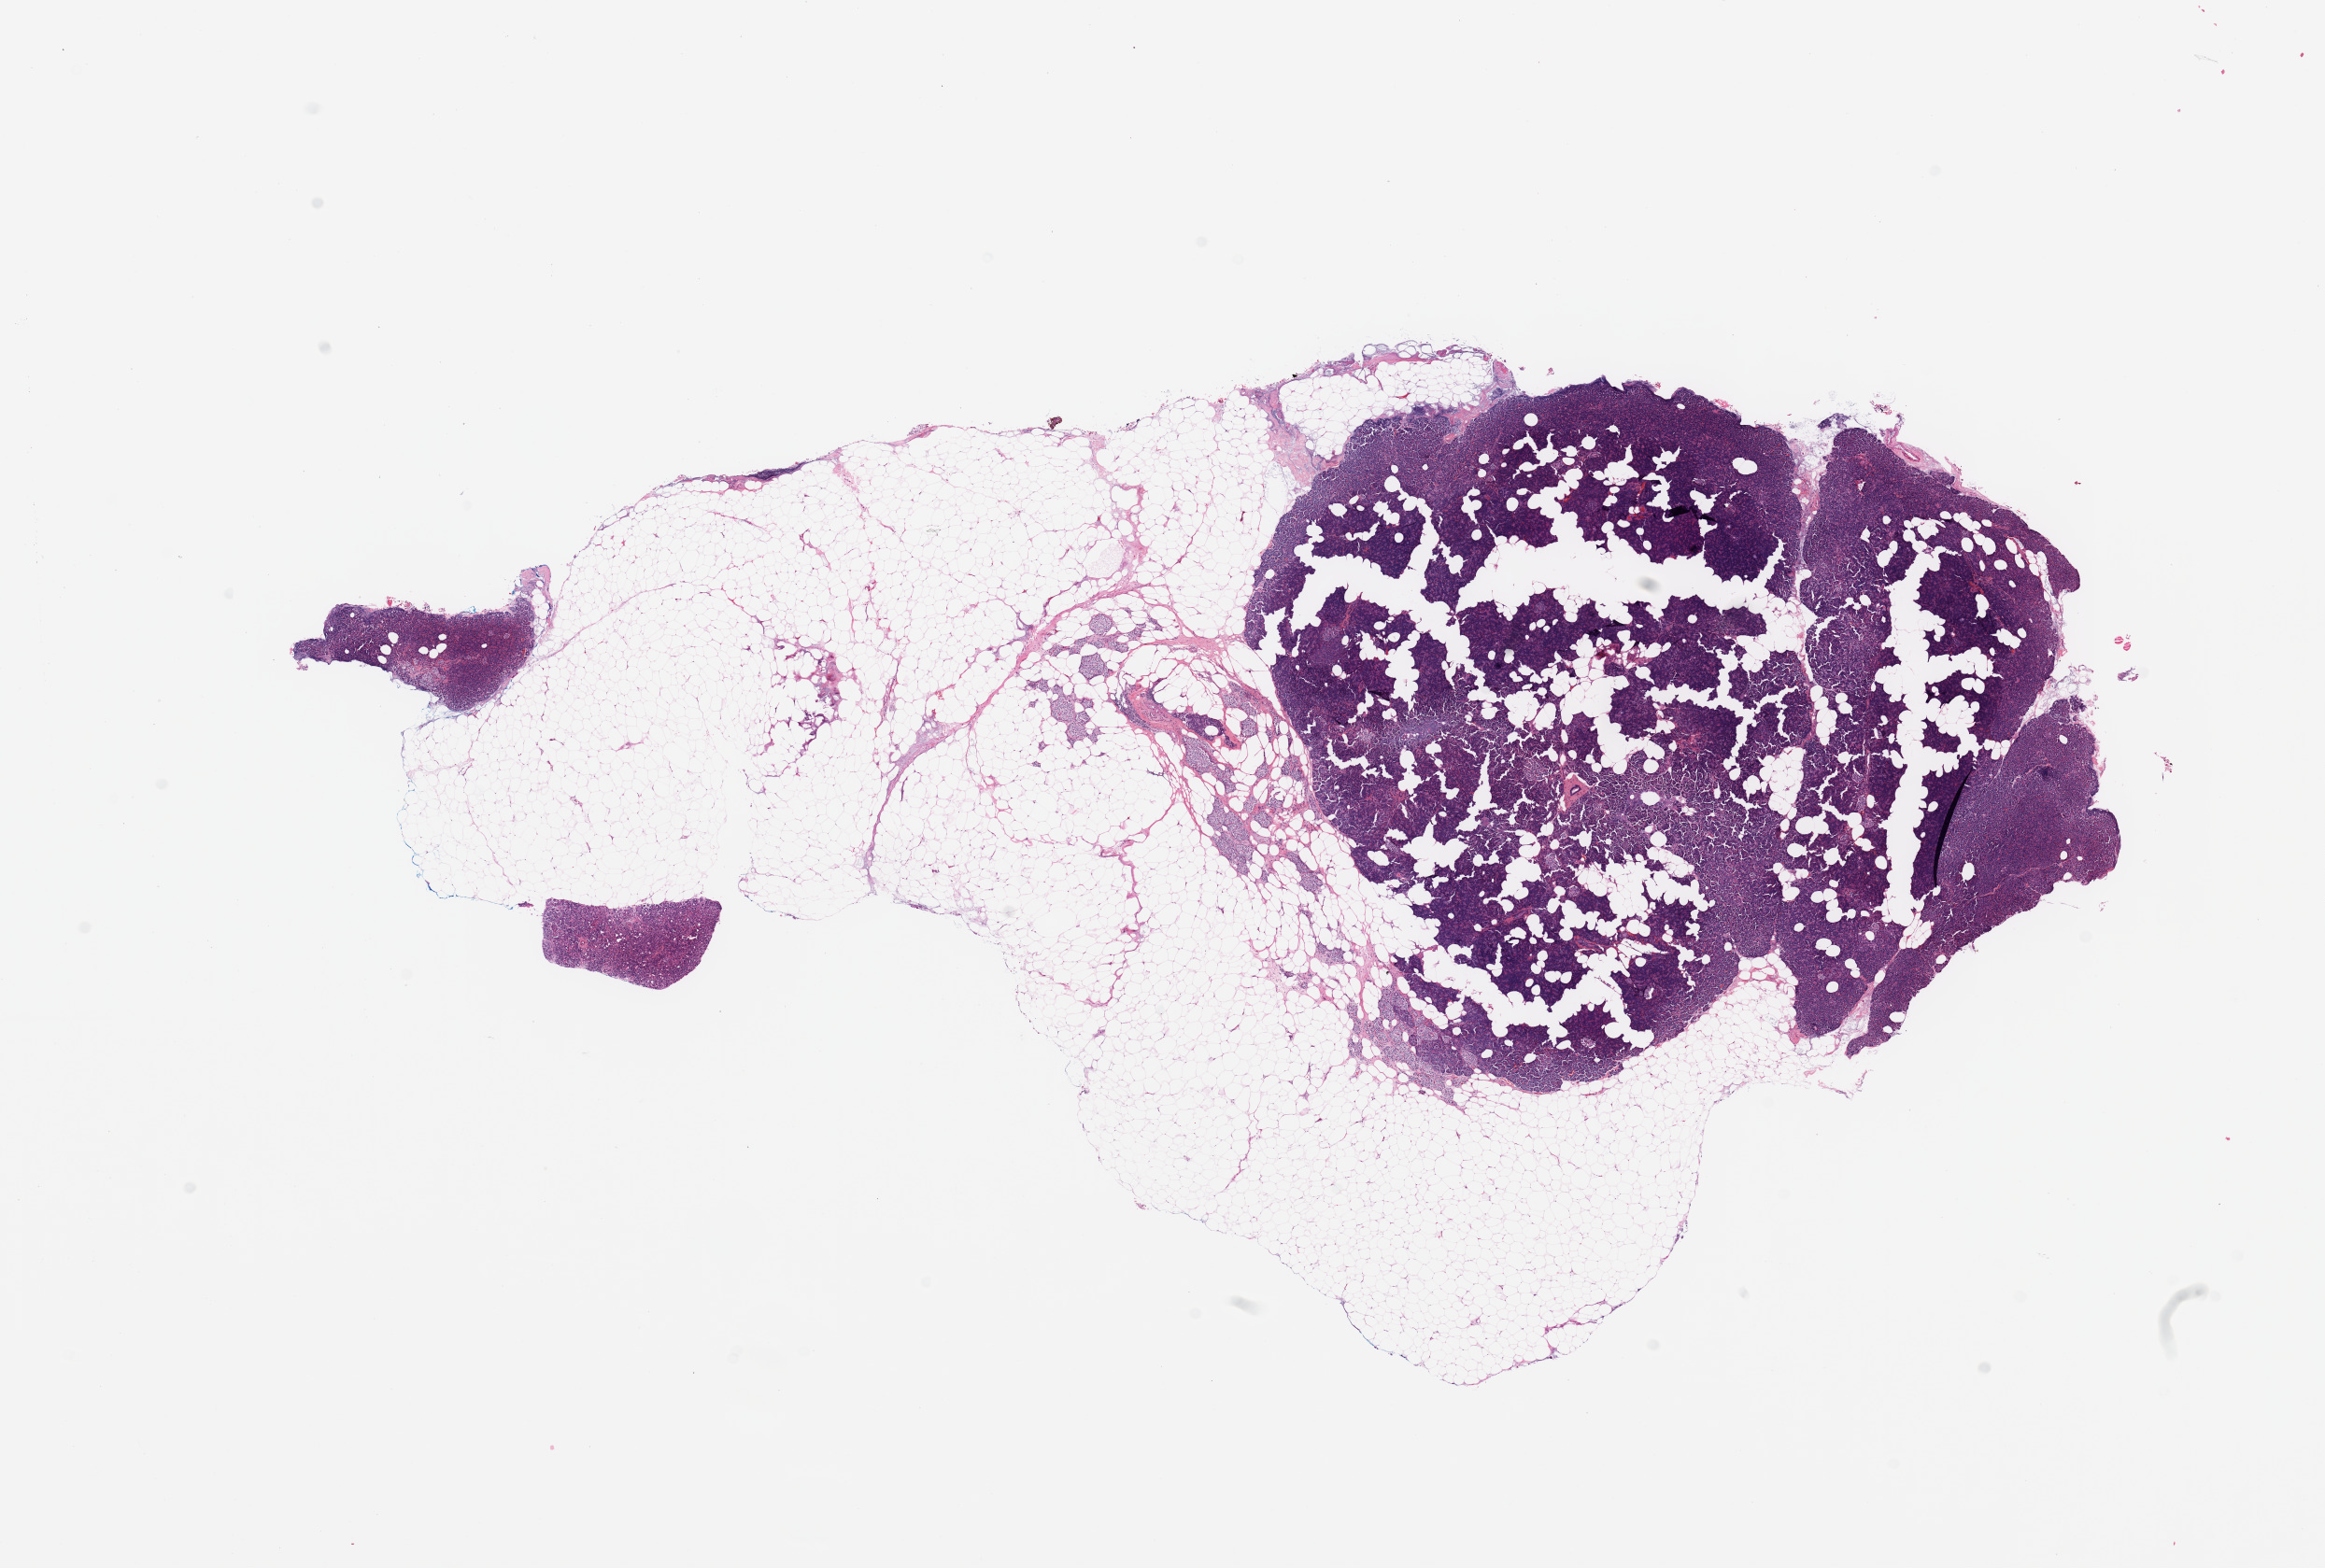
Whole-slide histology image, H&E — low-resolution overview of the scanned area, about 19.7 x 13.3 mm. Normal (non-tumour) tissue sample, sampled site: pancreas. Female, 52 y/o.
This section: normal (non-tumour) tissue from the same patient. Patient diagnosis: Infiltrating duct carcinoma, NOS.